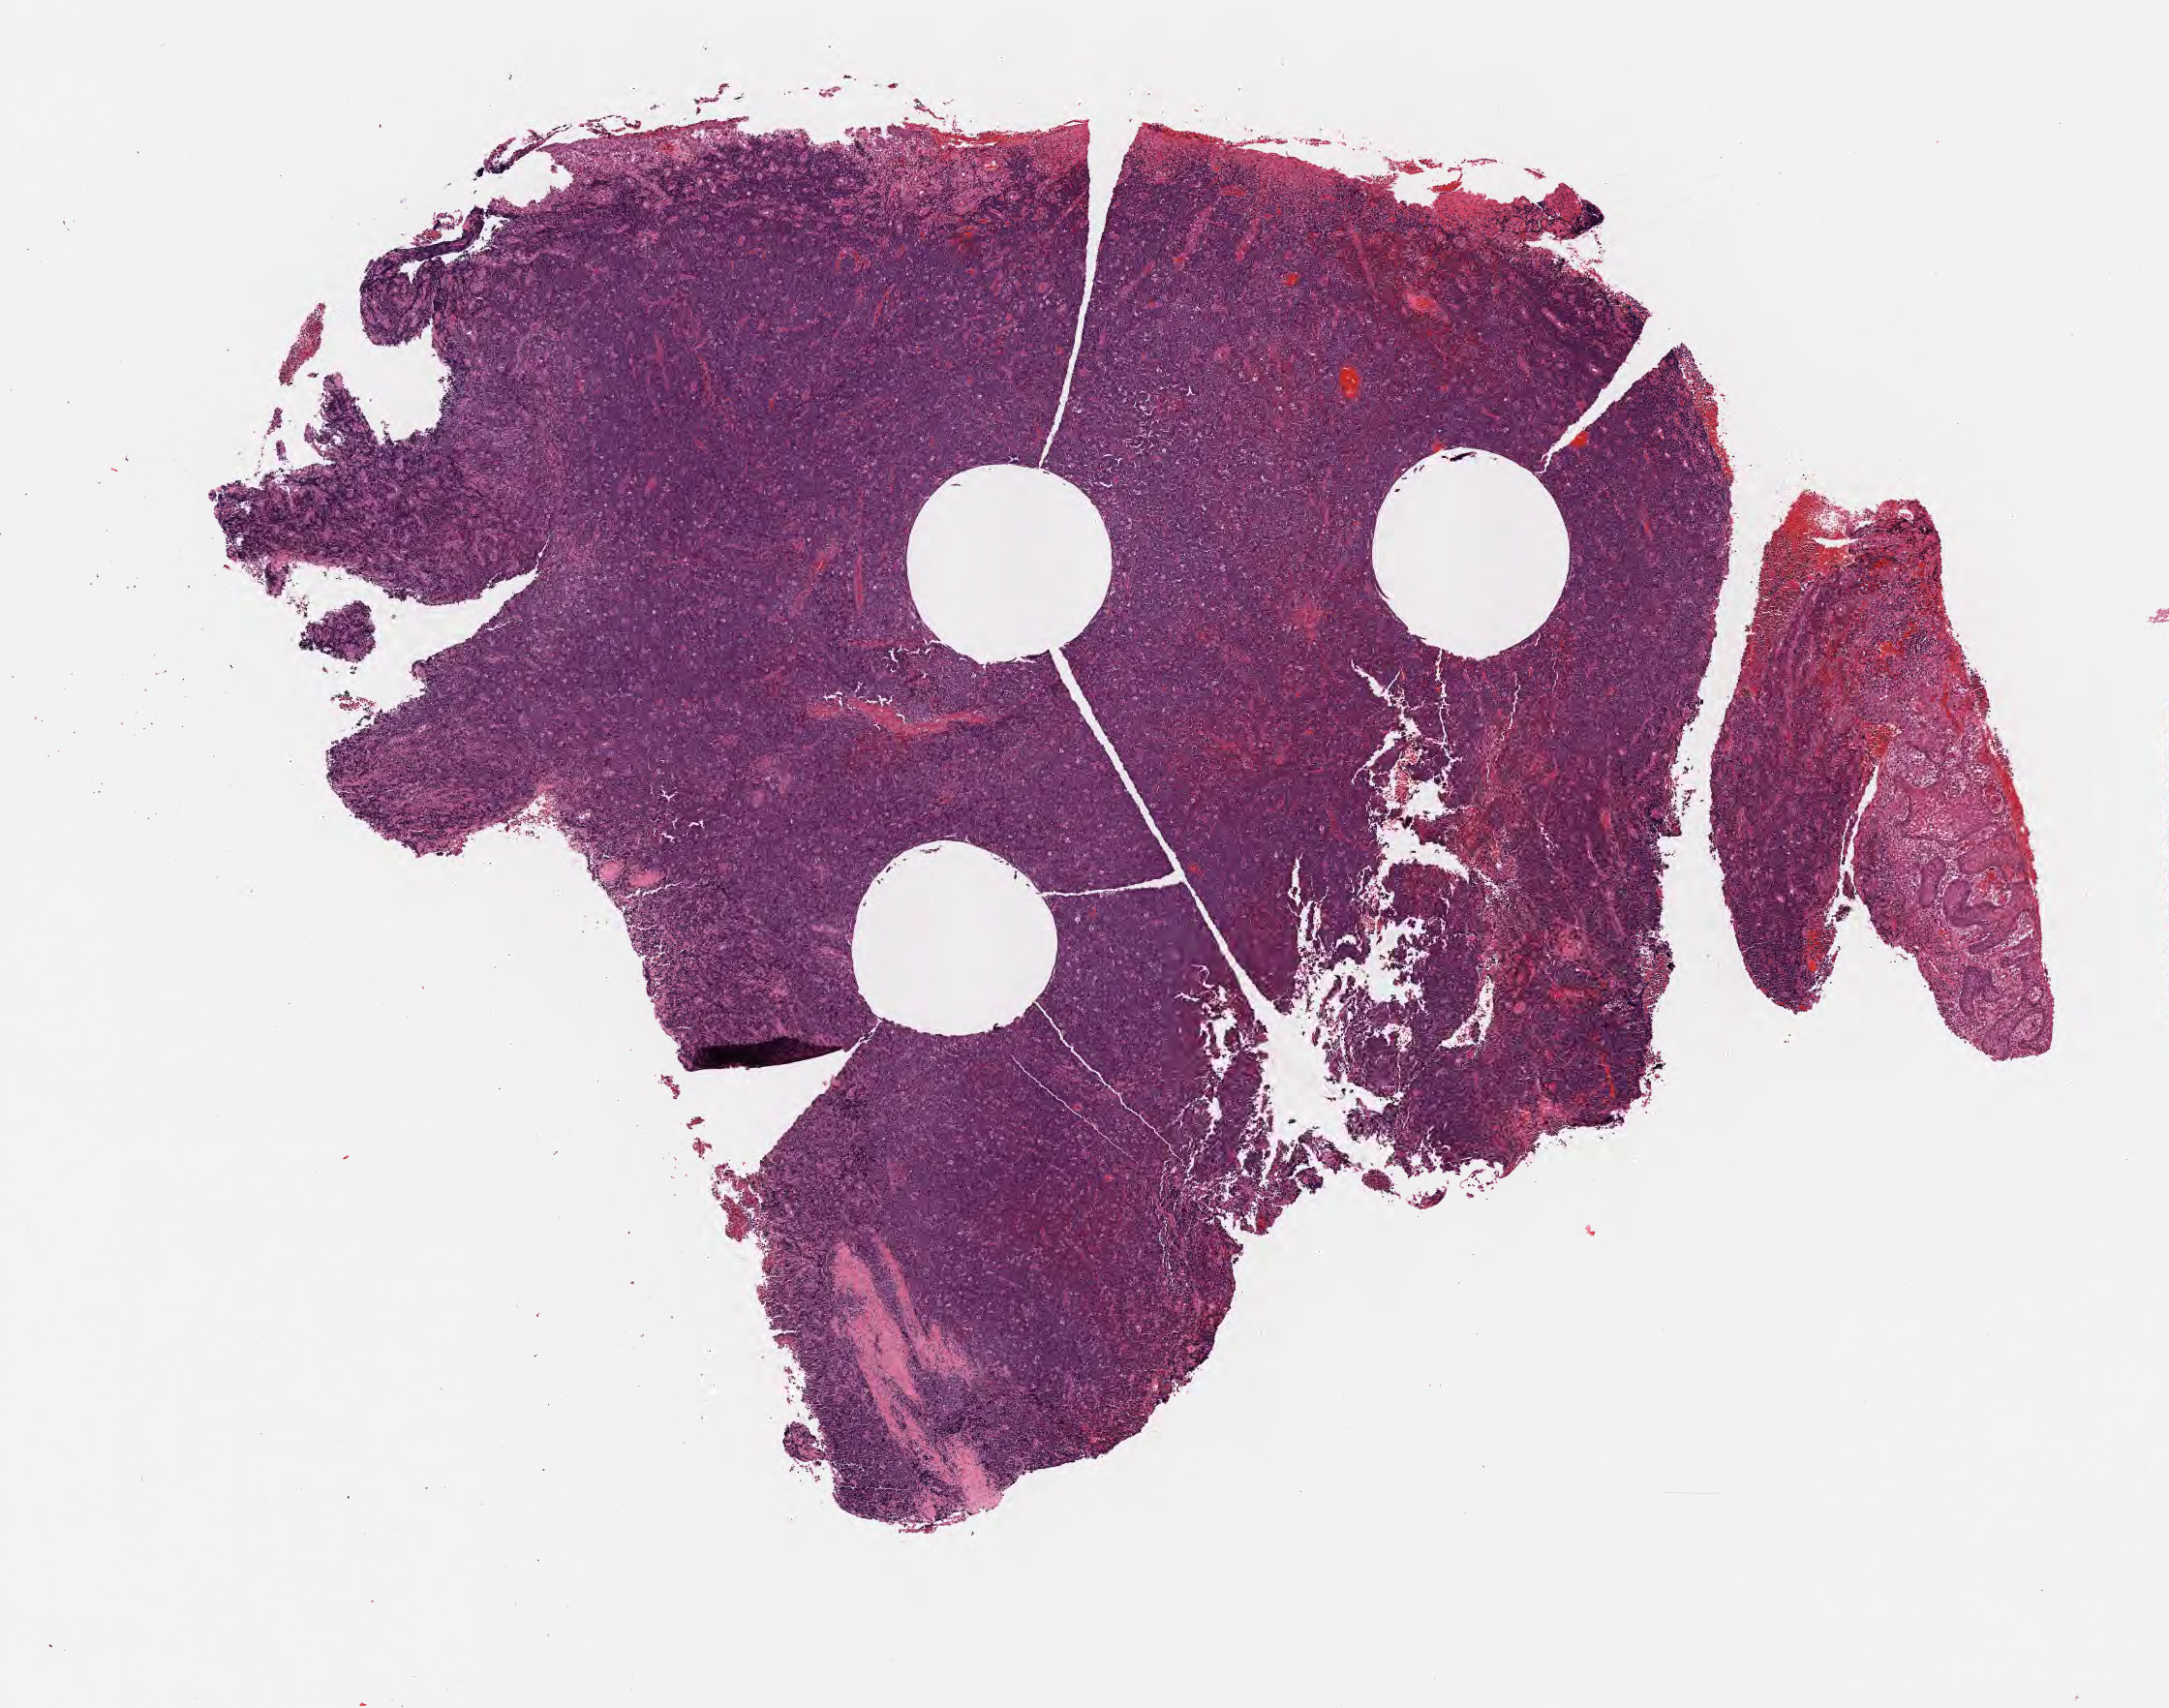
Hematoxylin and eosin (H&E) whole-slide image — a low-resolution overview of the entire scanned area, about 9.1 x 7.1 mm, FFPE section, primary tumor, anatomic site: mandible. Patient: male, age at initial diagnosis 4 years. Pathologist review of this section (percent, as recorded): tumor cells 85%, tumor nuclei 90%, stromal cells 5%, necrosis 5%, normal cells 5%. Inflammatory infiltration, as recorded: lymphocyte infiltration 30%, monocyte infiltration 30%, neutrophil infiltration 5%.
- section: top of the tissue portion
- Ann Arbor stage (patient): Stage I
- histologic diagnosis: Burkitt lymphoma, NOS